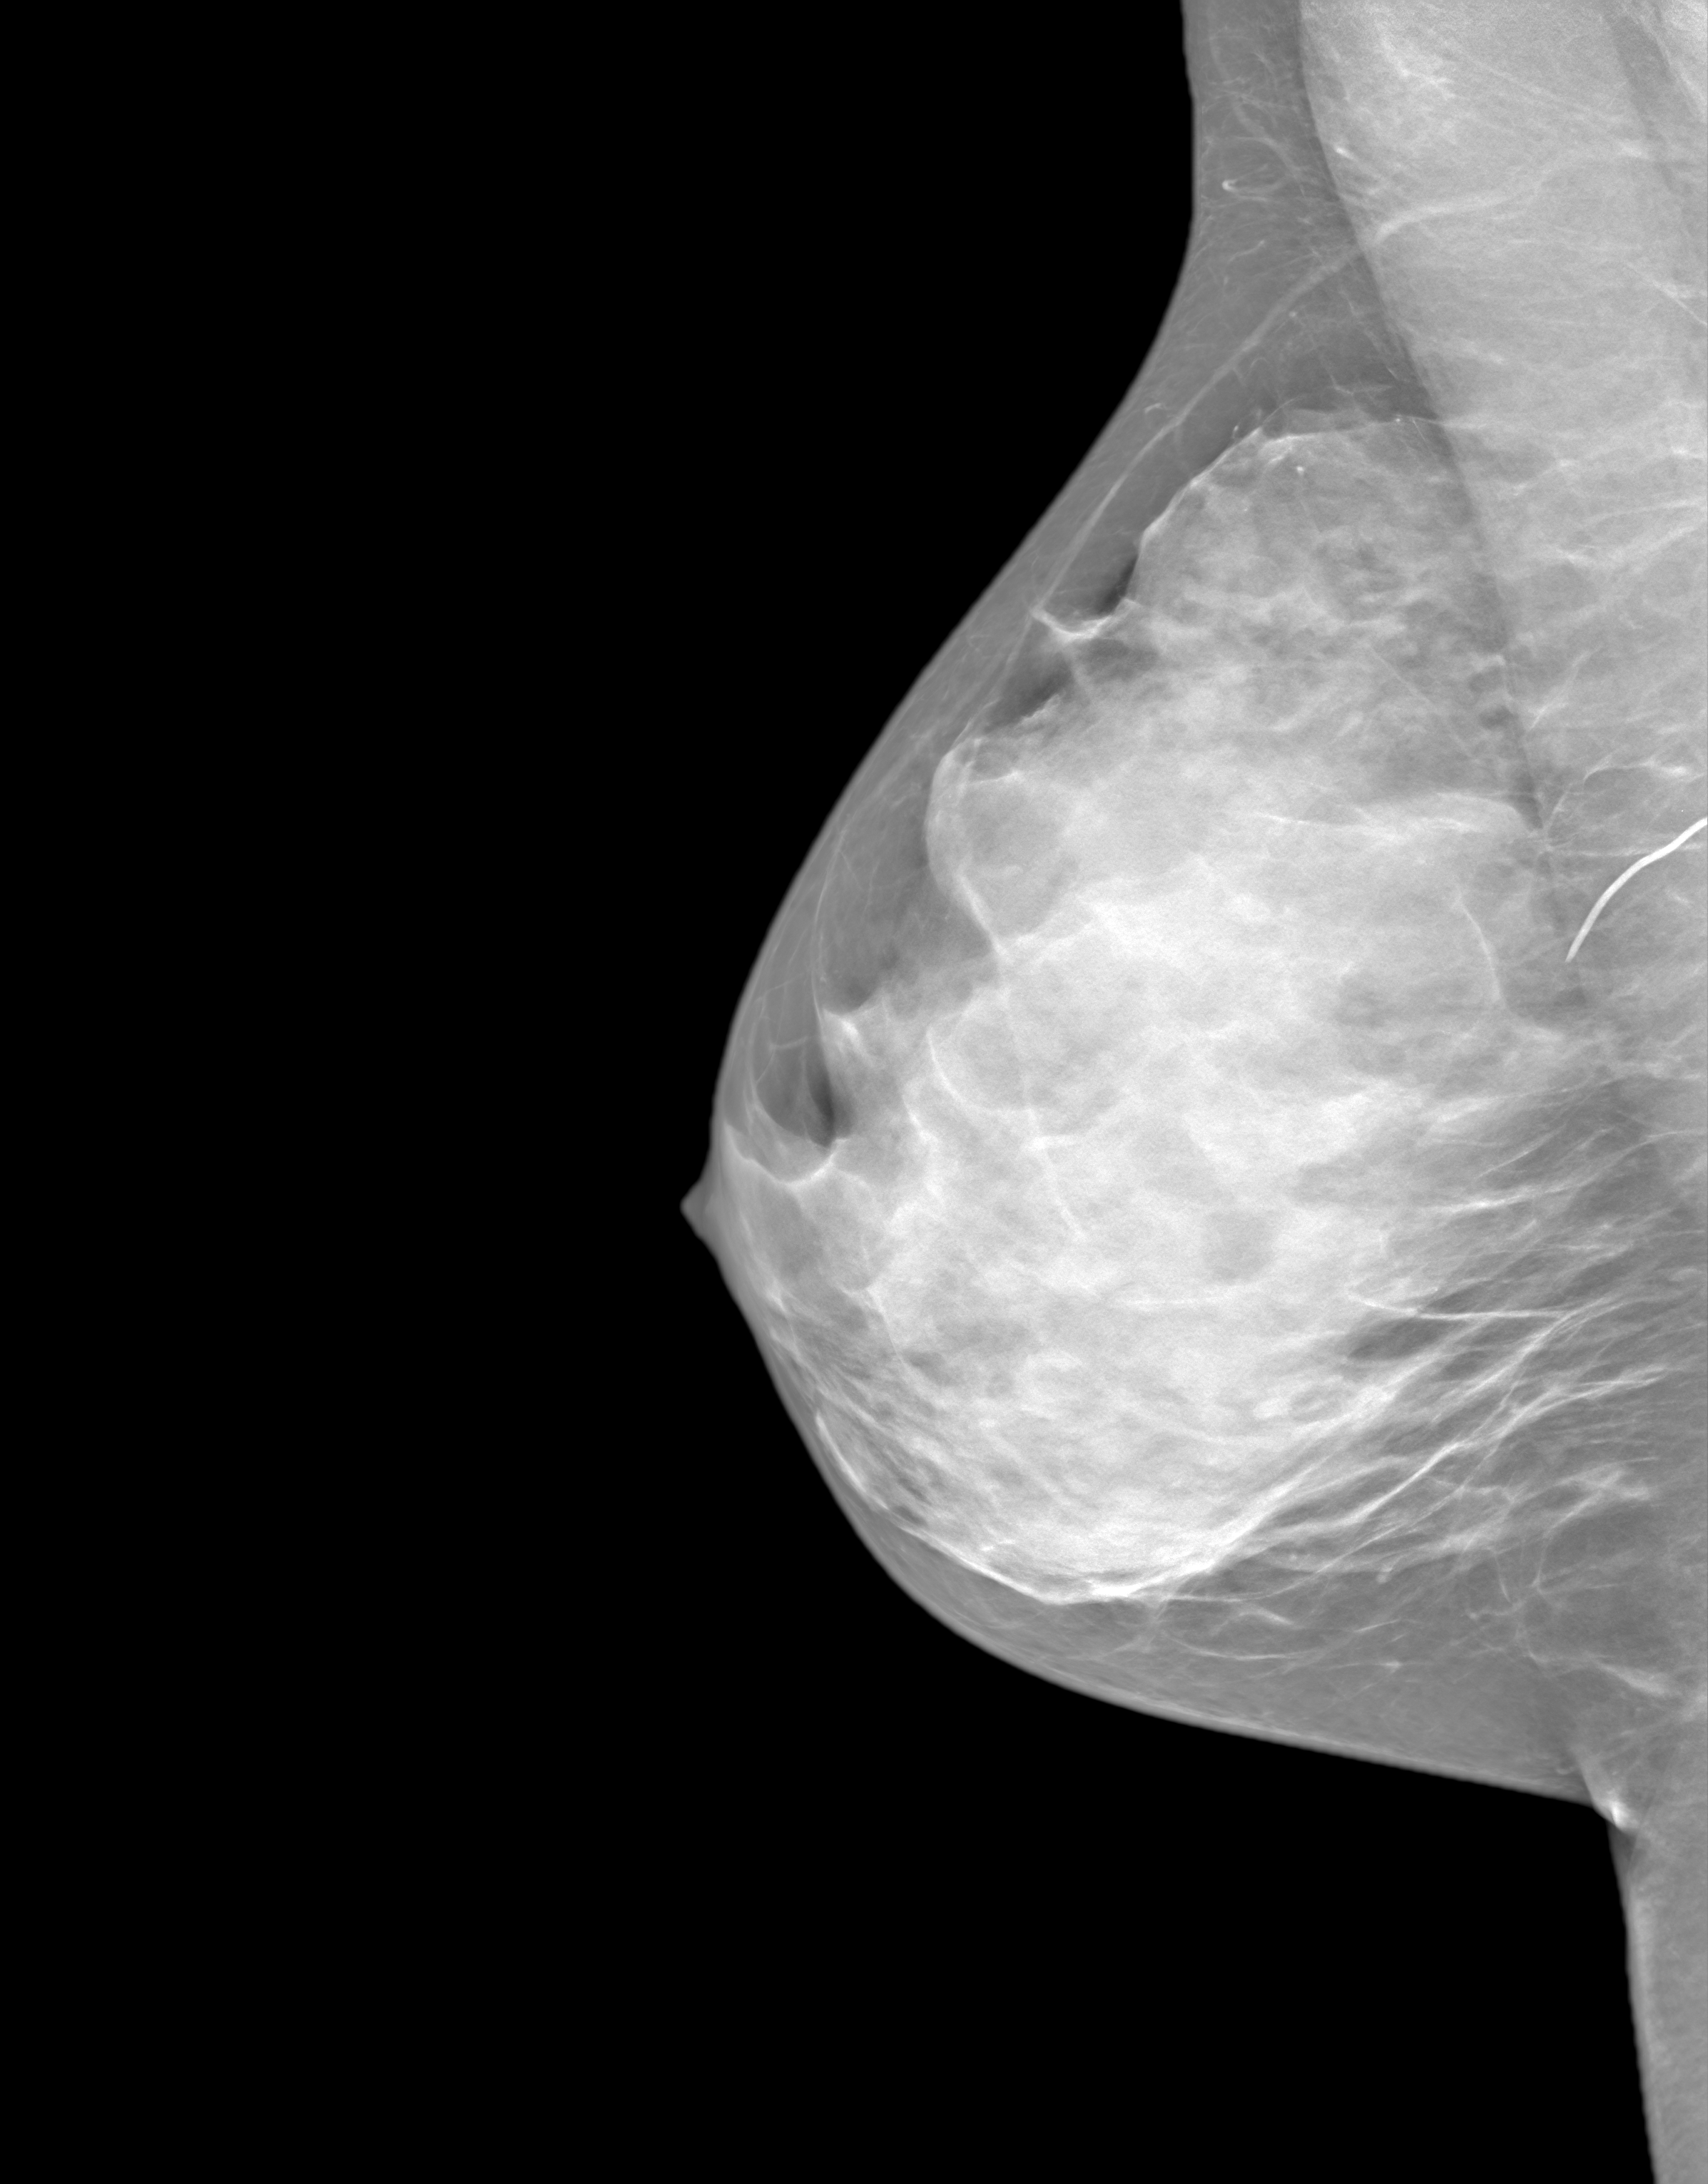
Synthetic 2-D view generated from a tomosynthesis acquisition (not an FFDM exposure), right breast, mediolateral oblique (MLO) view, annual screening mammography examination. Patient aged 43 years (female).
- breast density at the screening exam (both breasts): extremely dense (BI-RADS density category d)
- final BI-RADS category for the screening round (tomosynthesis exam, both breasts): category 1
- recall: no recall after this screen